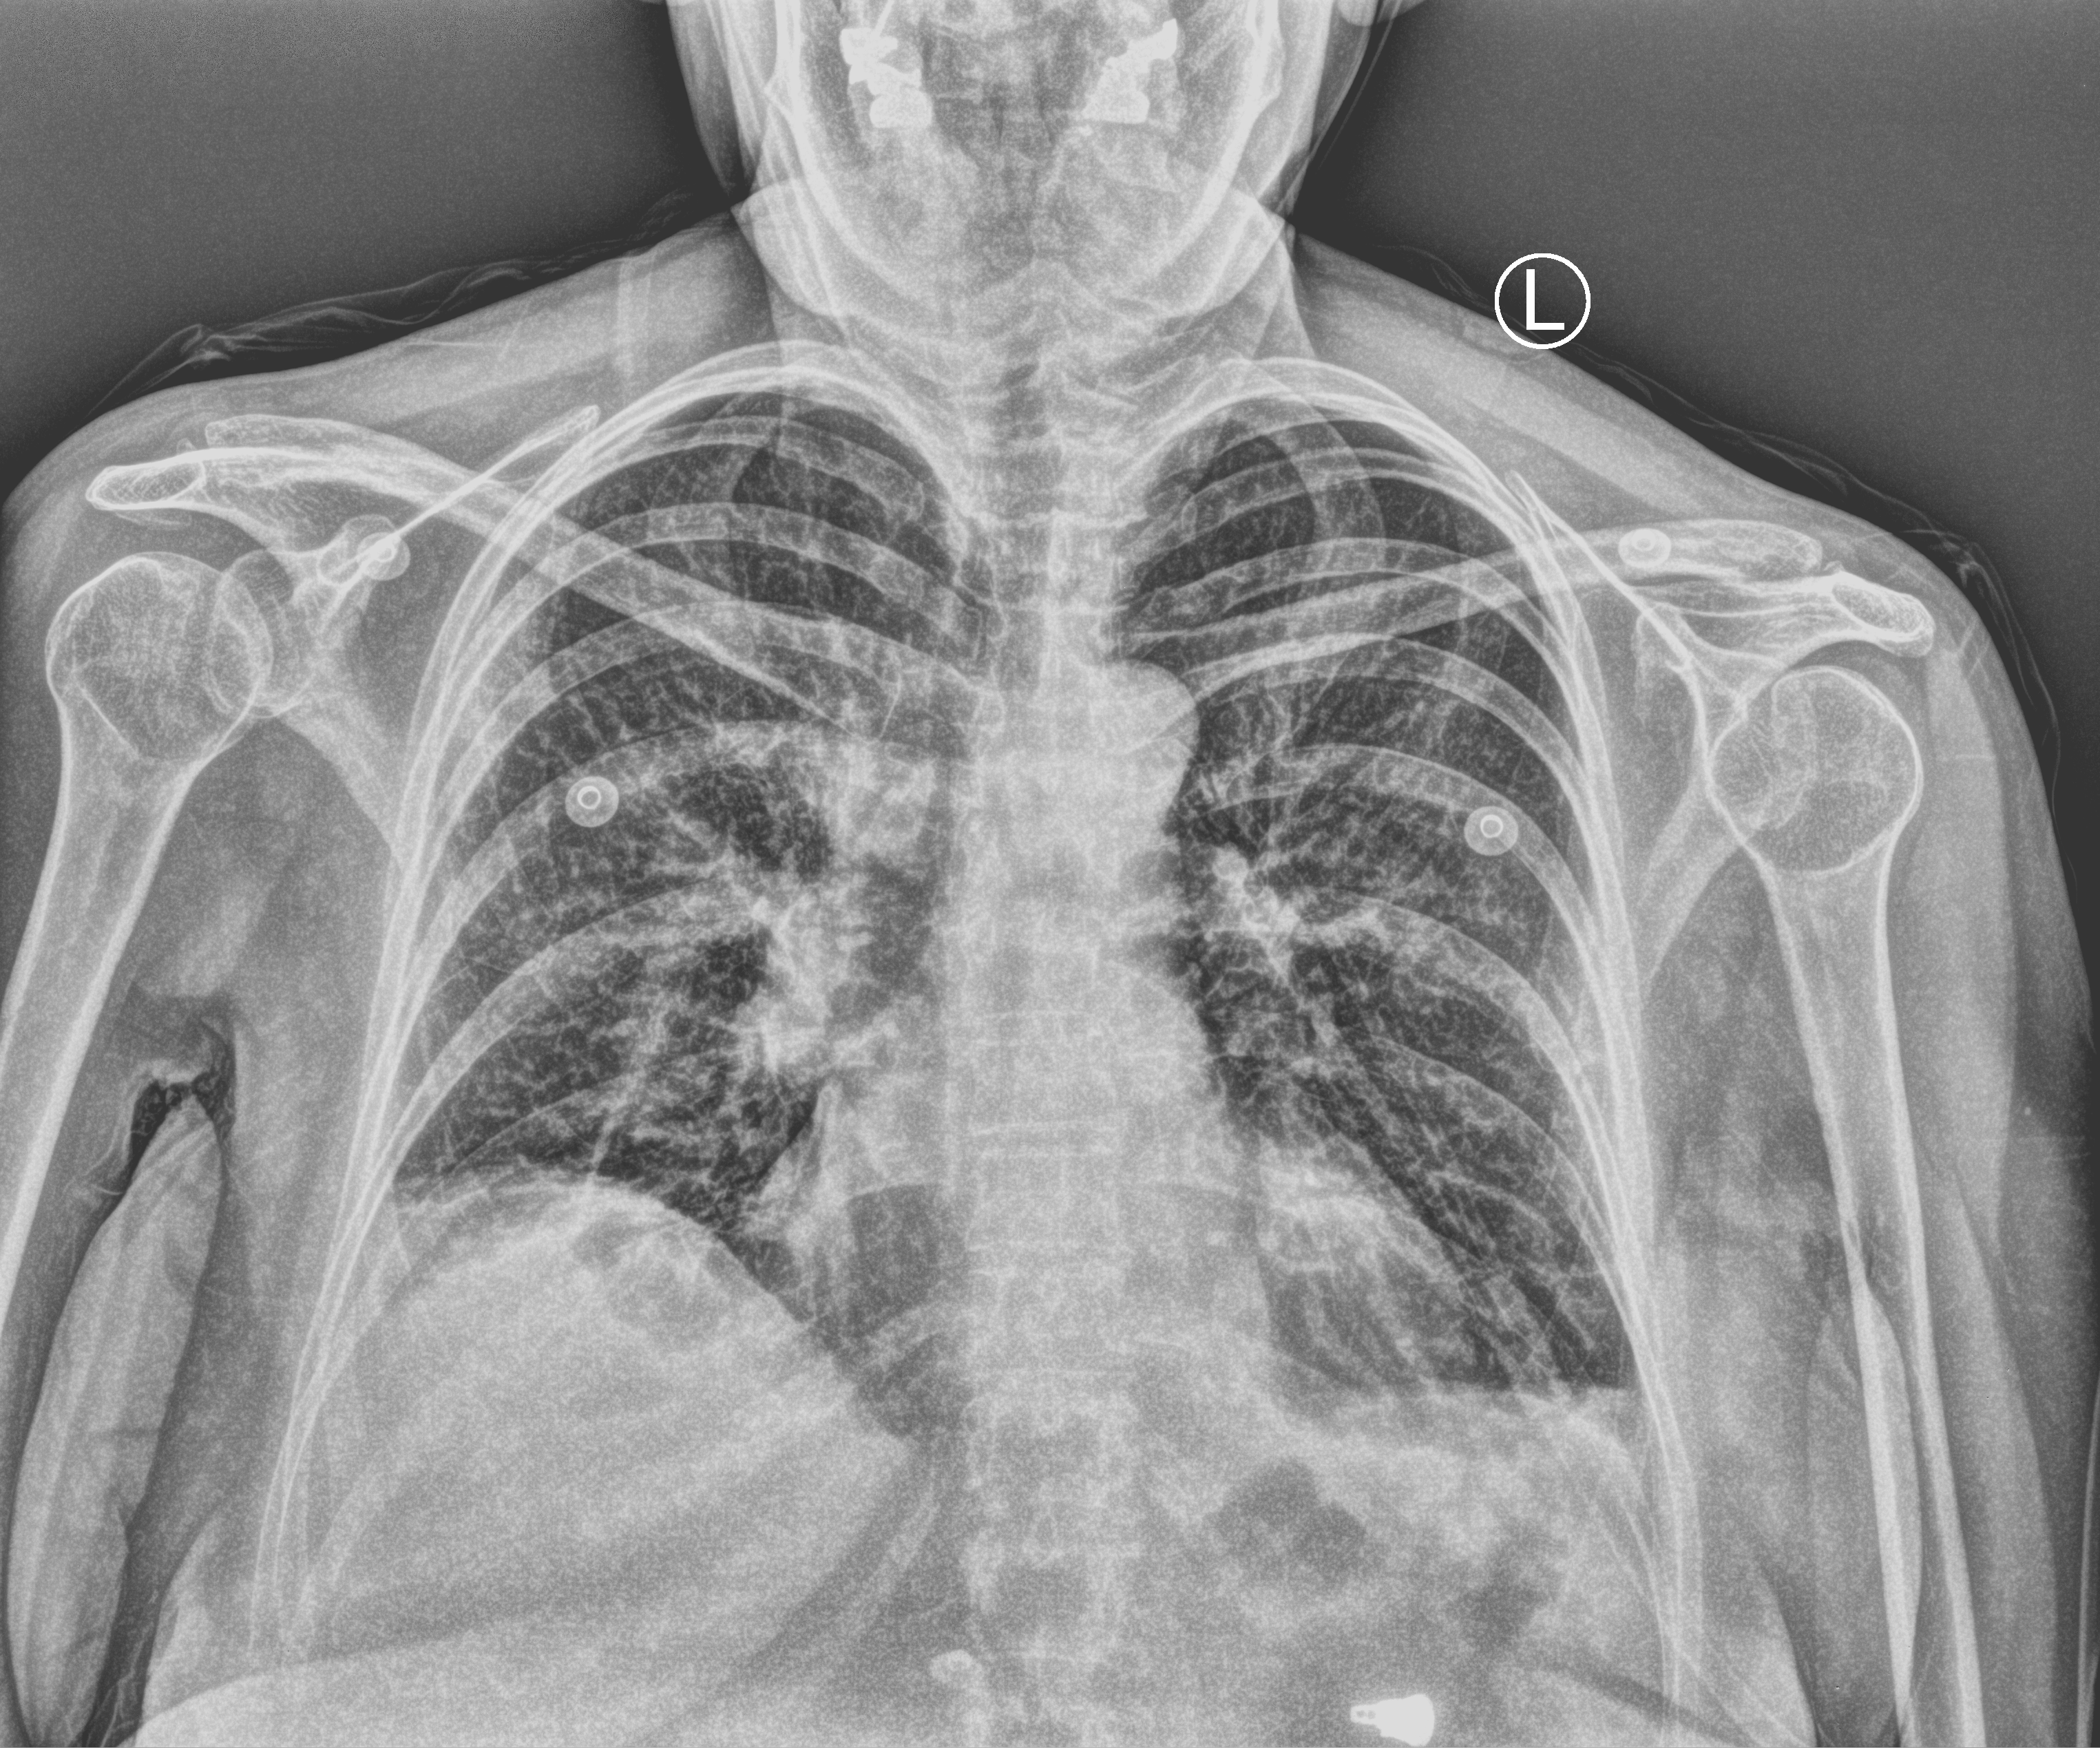
Bedside chest radiograph (computed radiography); anteroposterior (AP) projection. Female patient hospitalised with COVID-19, age 60–74 years.
Admission-level facts for this patient (not findings on this image; timing relative to this image not recorded):
- smoking status (admission record): never